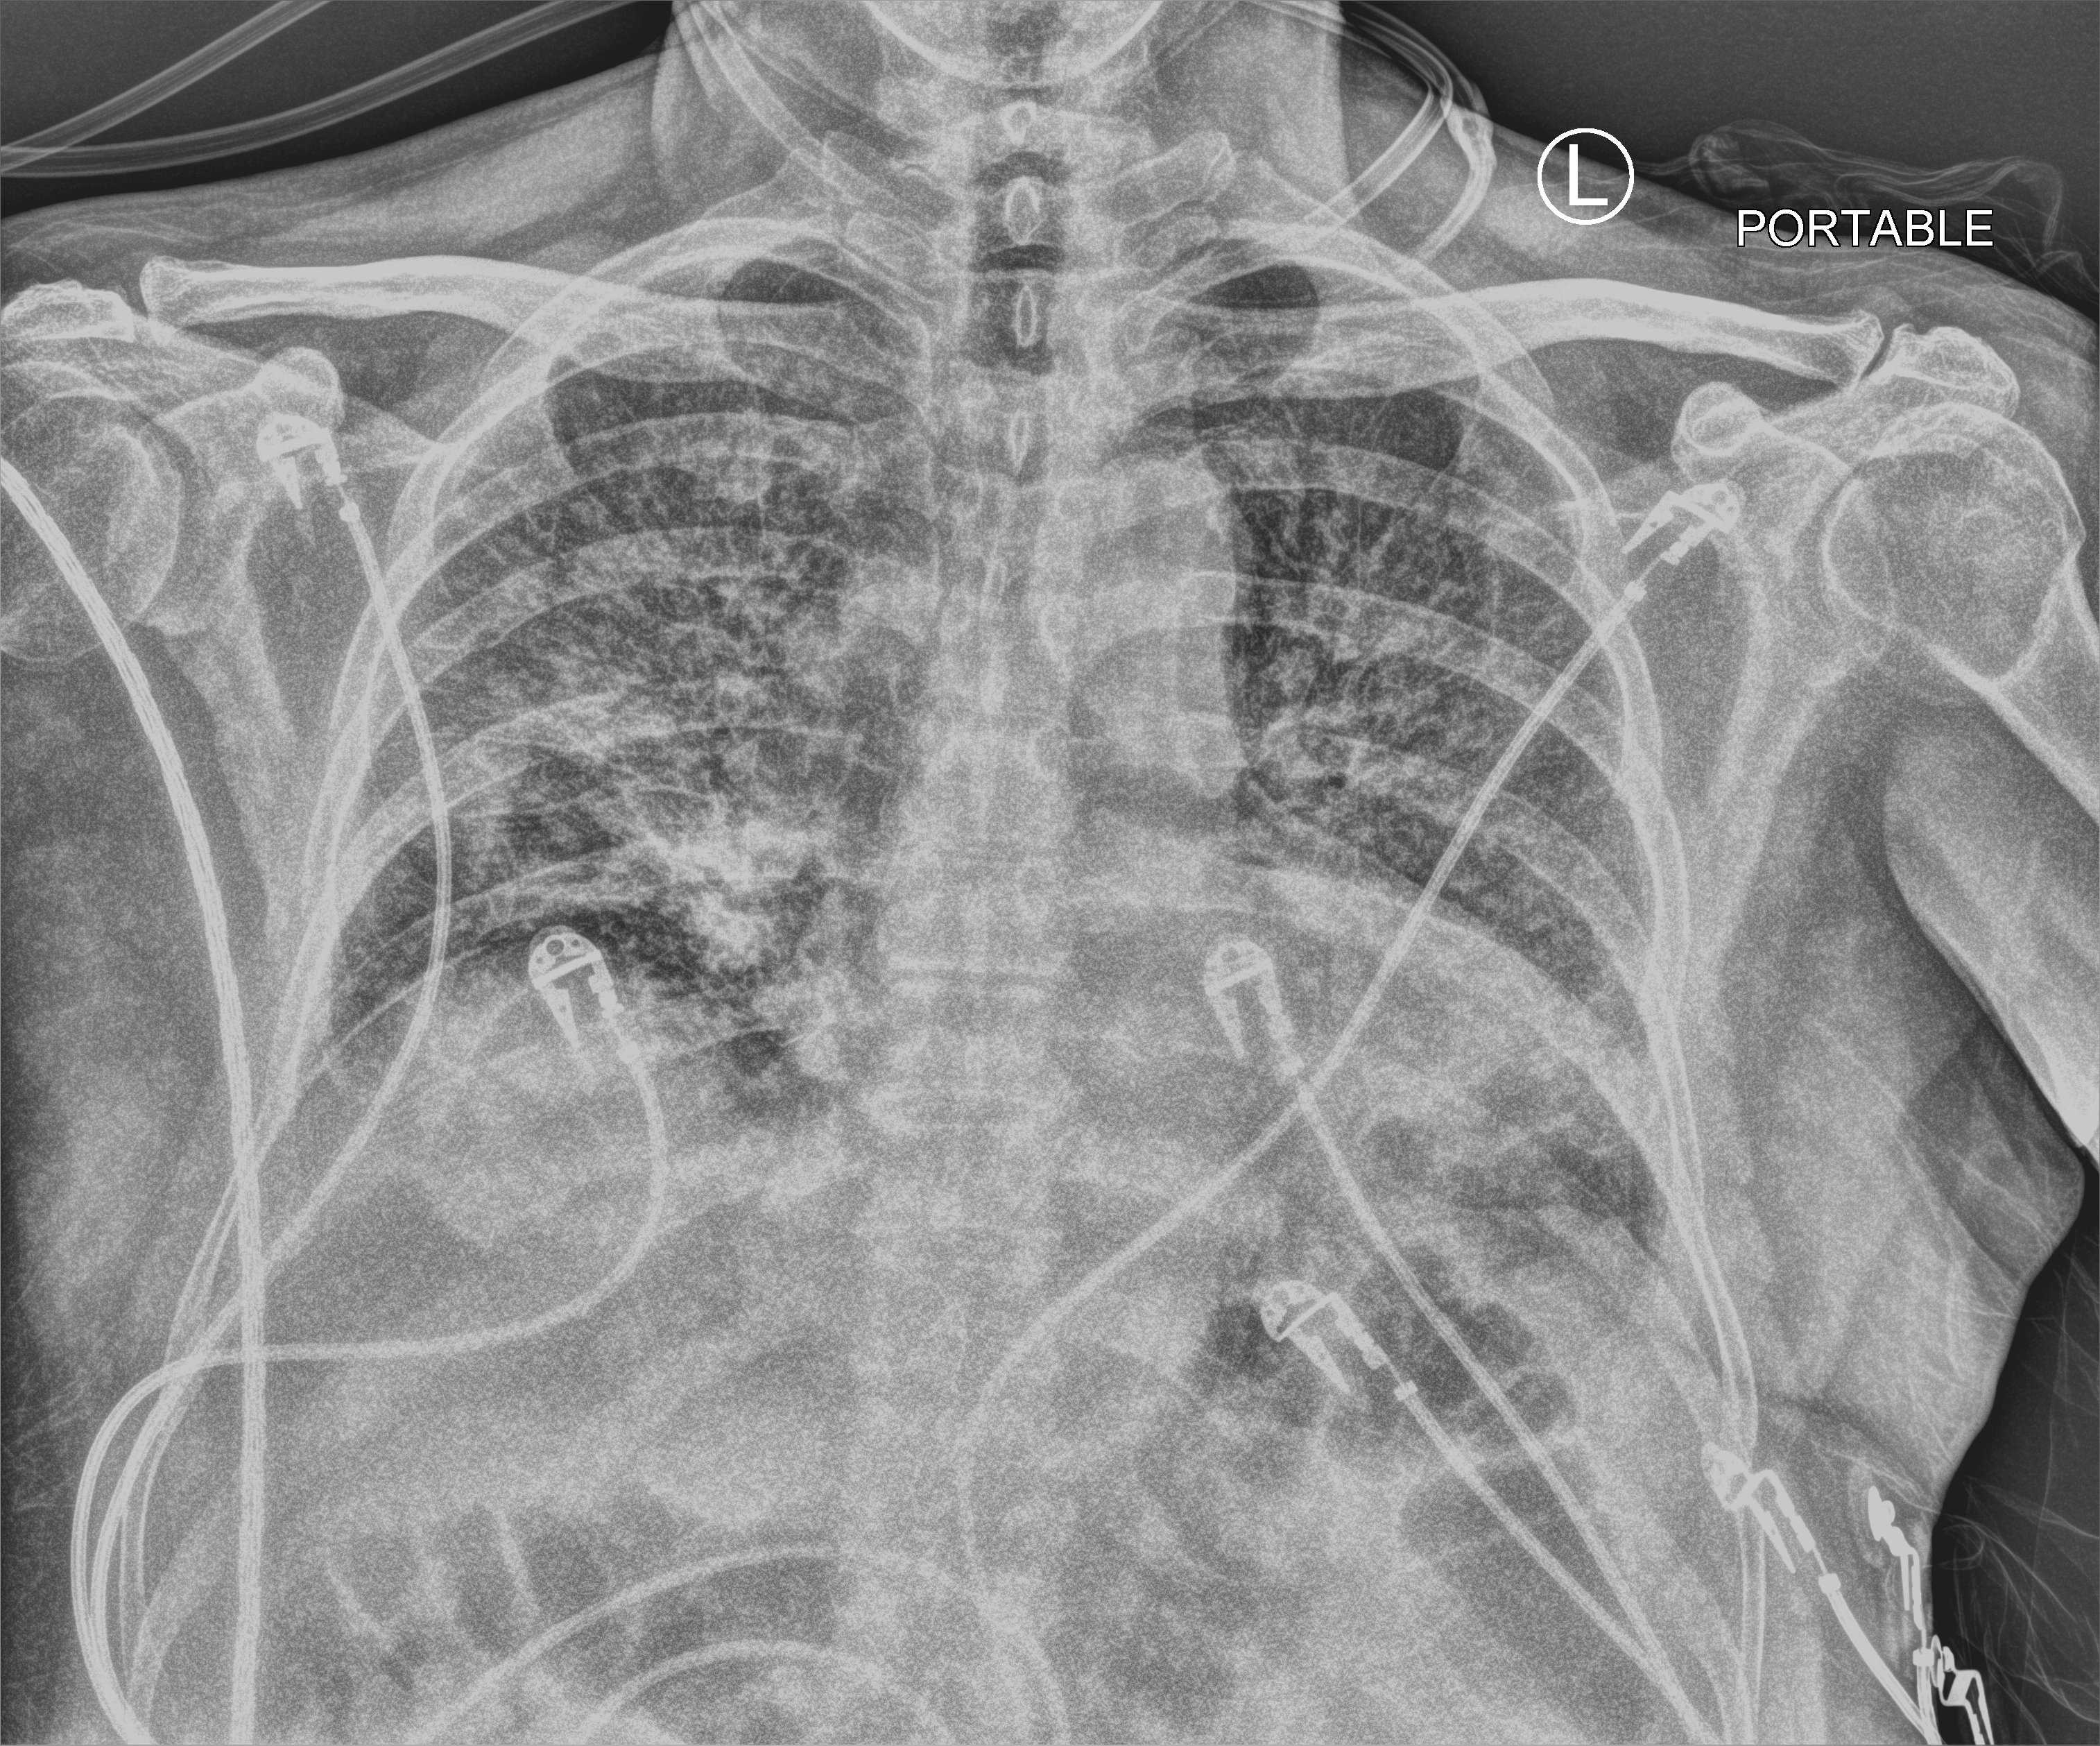
Chest X-ray (portable). Patient hospitalised with COVID-19; male, aged 60–74 years.
From the hospital-stay record, not from the radiograph (when in the stay this image was taken is not recorded): admitted to intensive care during this hospital stay: yes; diabetes (admission record): no.